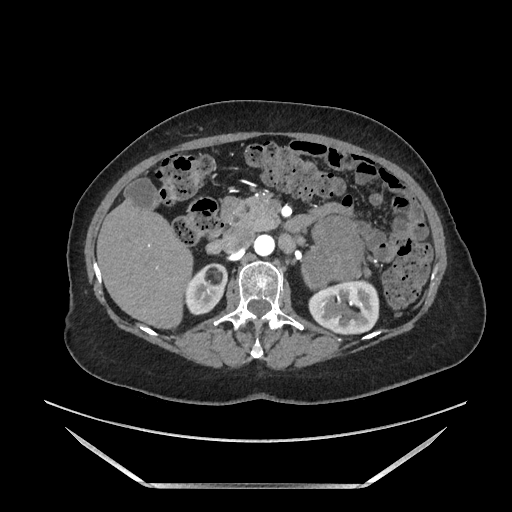
Contrast-enhanced abdominal CT, one axial slice. Slice 90 of 205 in the series (ordered by position). Soft-tissue window (W 400 / L 40 HU). 1.25 mm slice thickness. 512 × 512 image matrix, field of view 440 × 440 mm. Female patient. Case-level facts recorded for this patient, not image findings: diagnosis: adrenocortical carcinoma; tumour side: left adrenal; tumour size at pathology: 12.5 cm; Ki-67 index: 39 %; stage (as recorded): 3.
Outlined on this slice (semi-automatically segmented with operator editing):
- mass: bounding box [x1, y1, x2, y2] px = [303, 217, 362, 288]